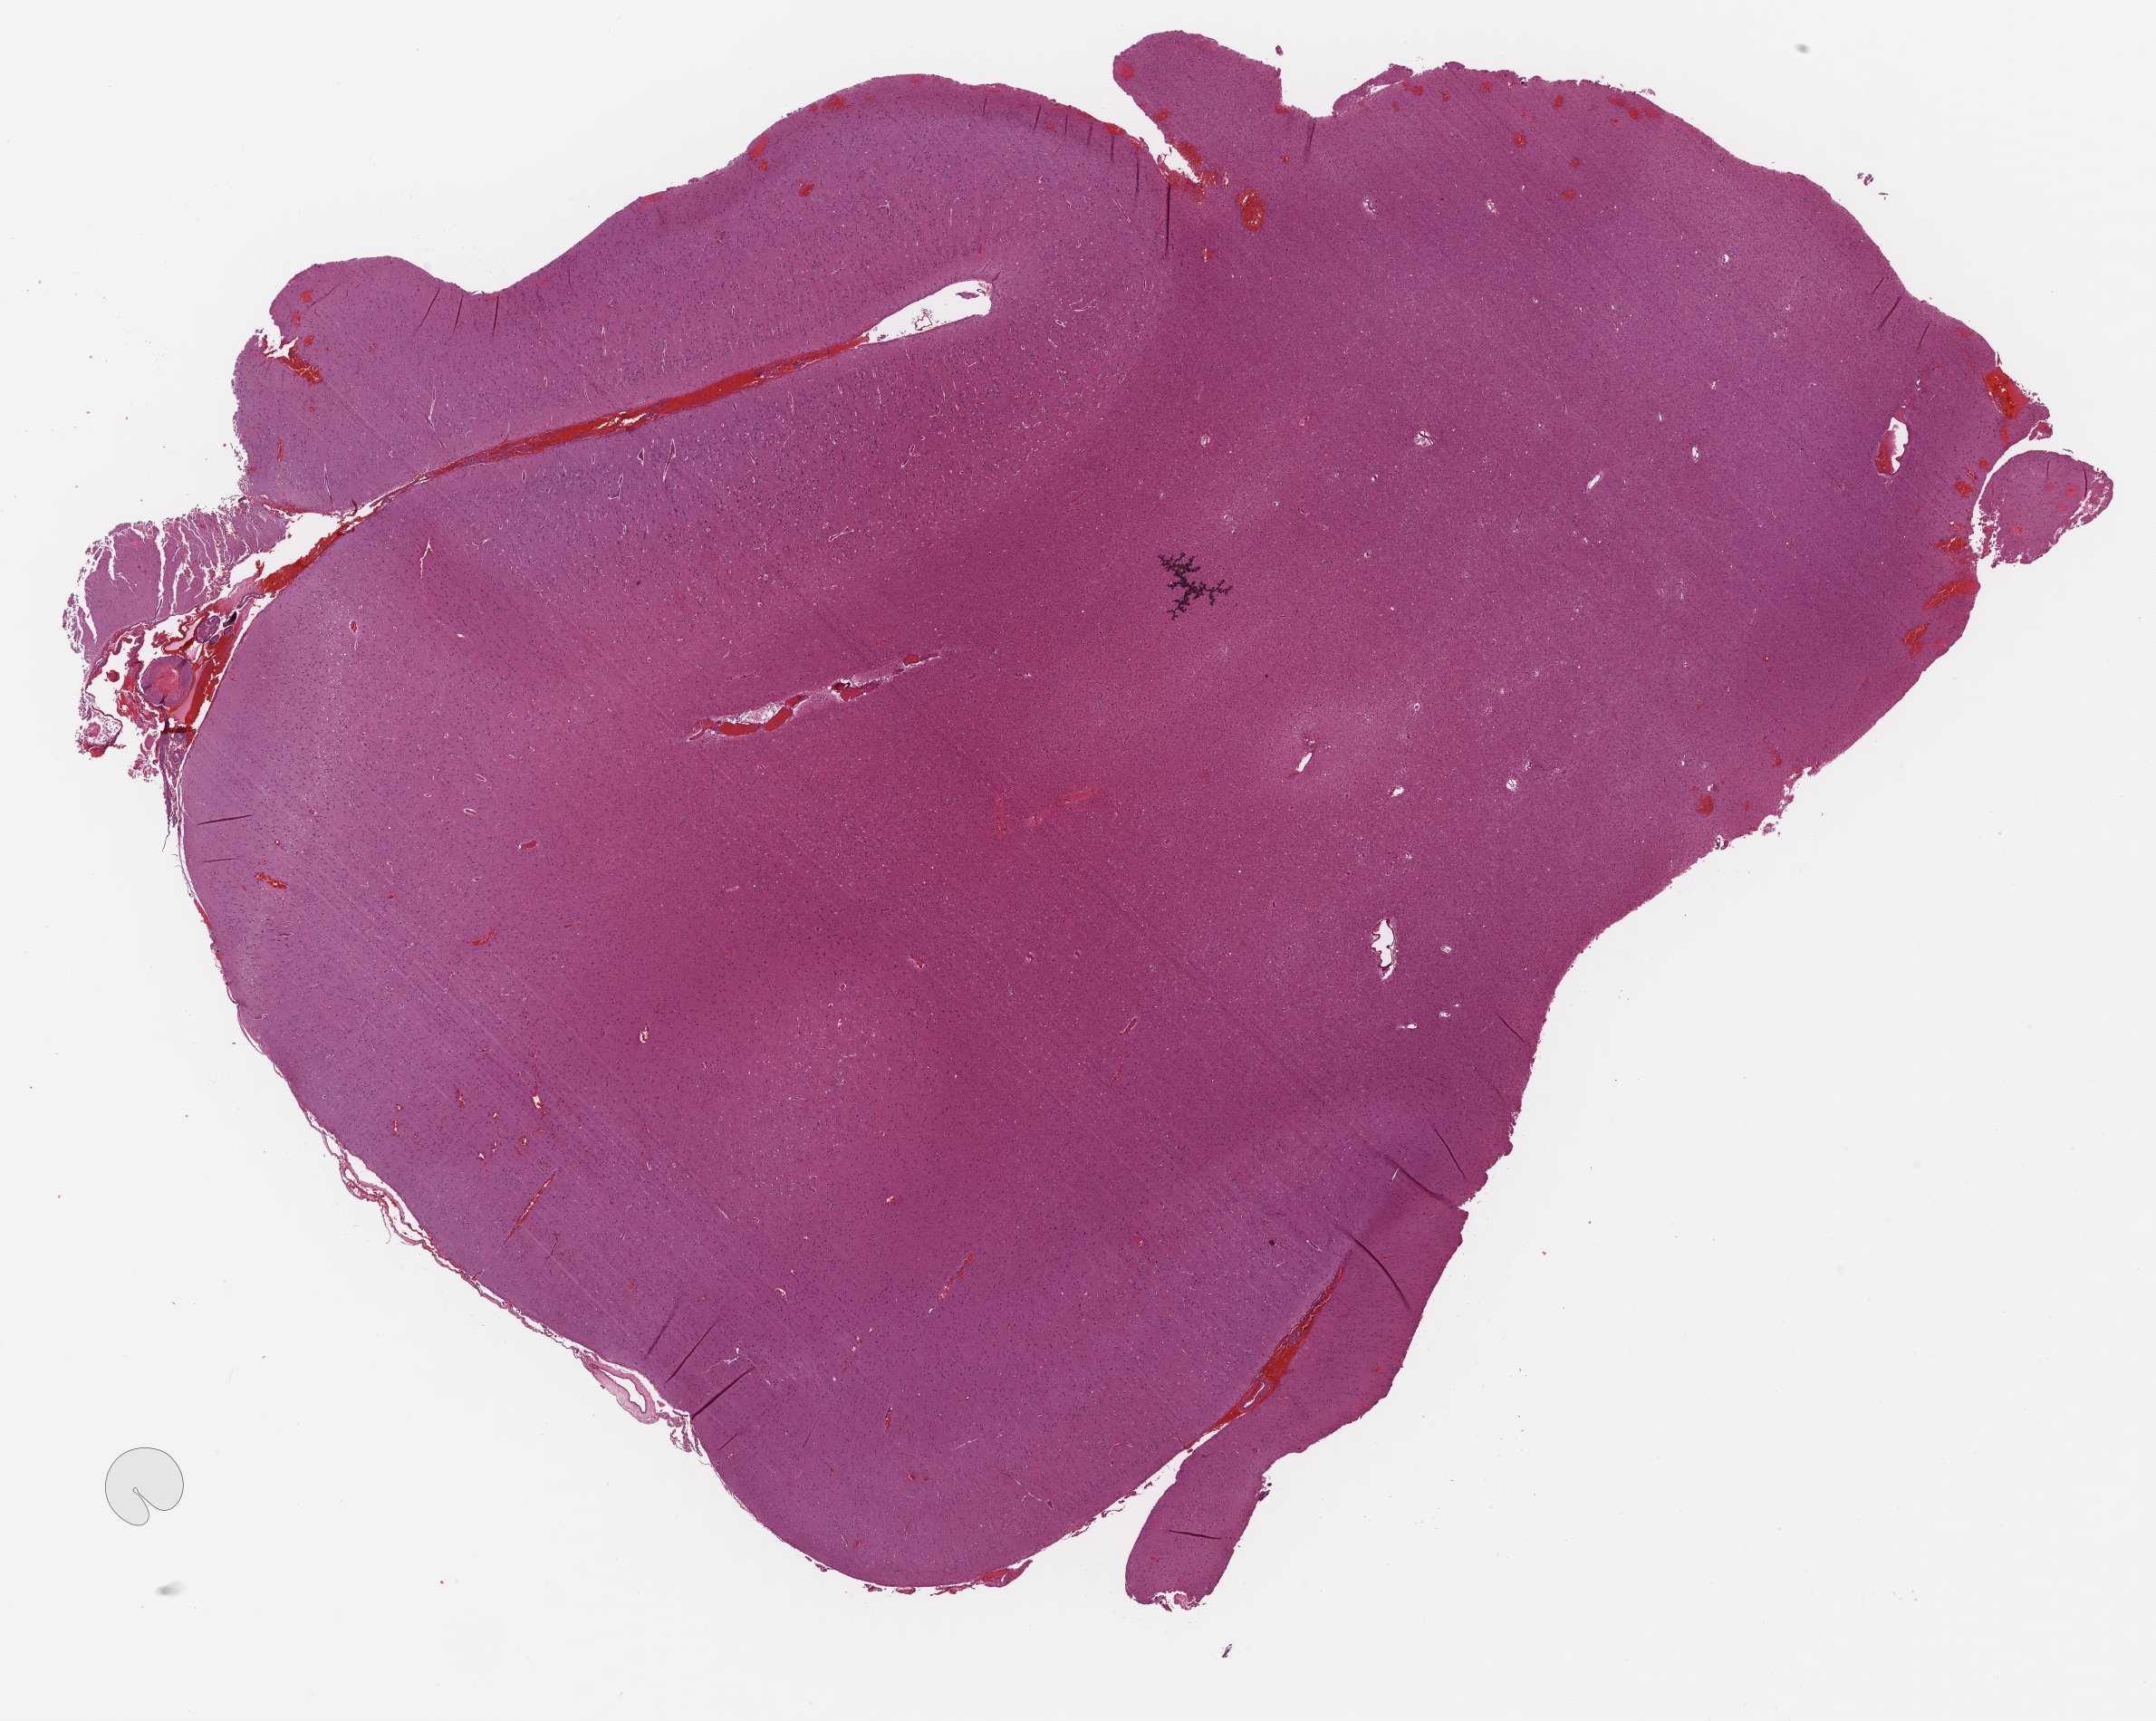
Digitized H&E tissue section (whole slide) — shown as a low-resolution overview of the whole scanned area (about 18.7 x 14.9 mm), formalin-fixed paraffin-embedded (FFPE) diagnostic section, brain, primary tumour sample. Patient: female, age at initial diagnosis 61 years.
Pathologic diagnosis: Astrocytoma, NOS.